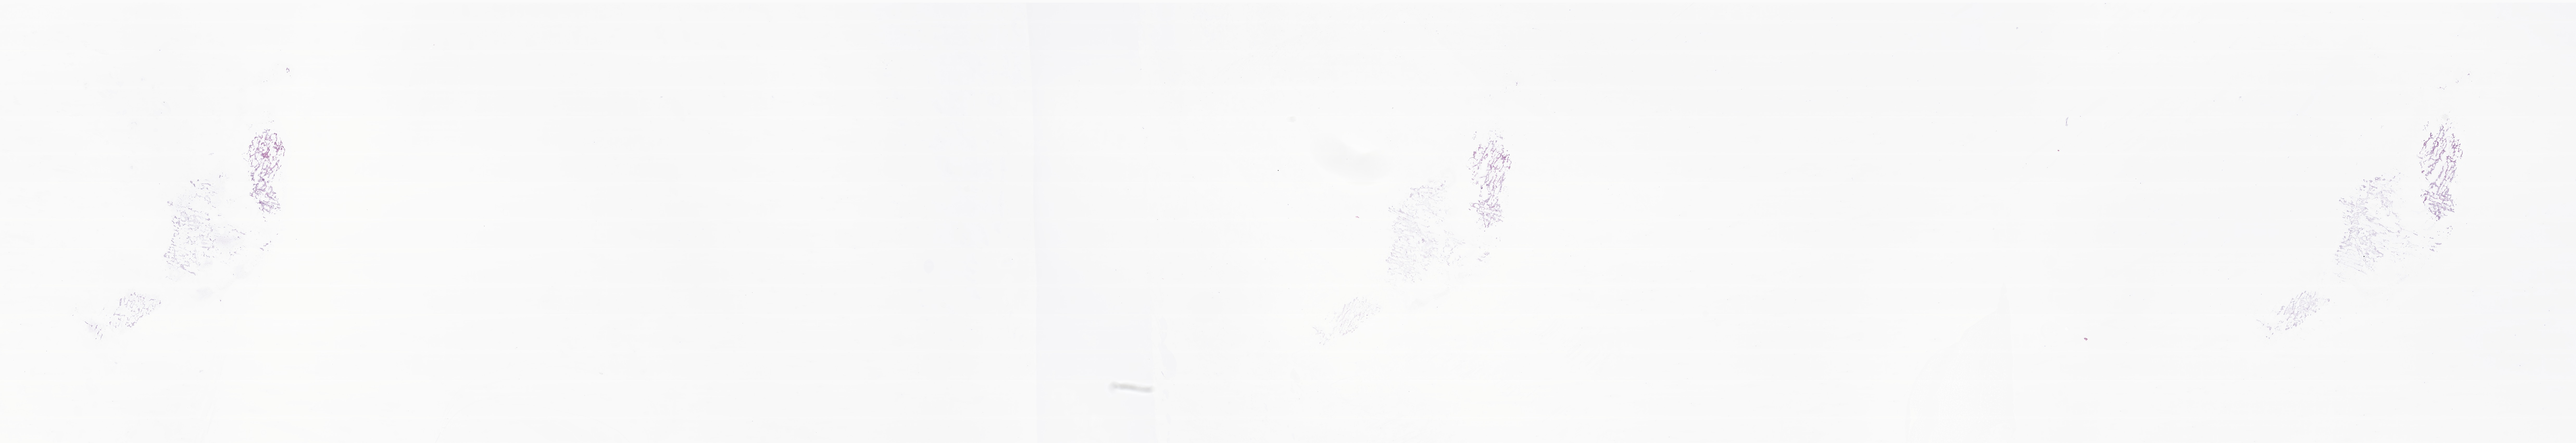
Whole-slide image, haematoxylin and eosin stain of tumor tissue from the brain — a low-resolution overview of the entire scanned area, about 41.7 x 7.2 mm; frozen section (OCT-embedded). Patient: male, age 161 months (13 years 5 months).
* diagnosis: Ganglioglioma, NOS